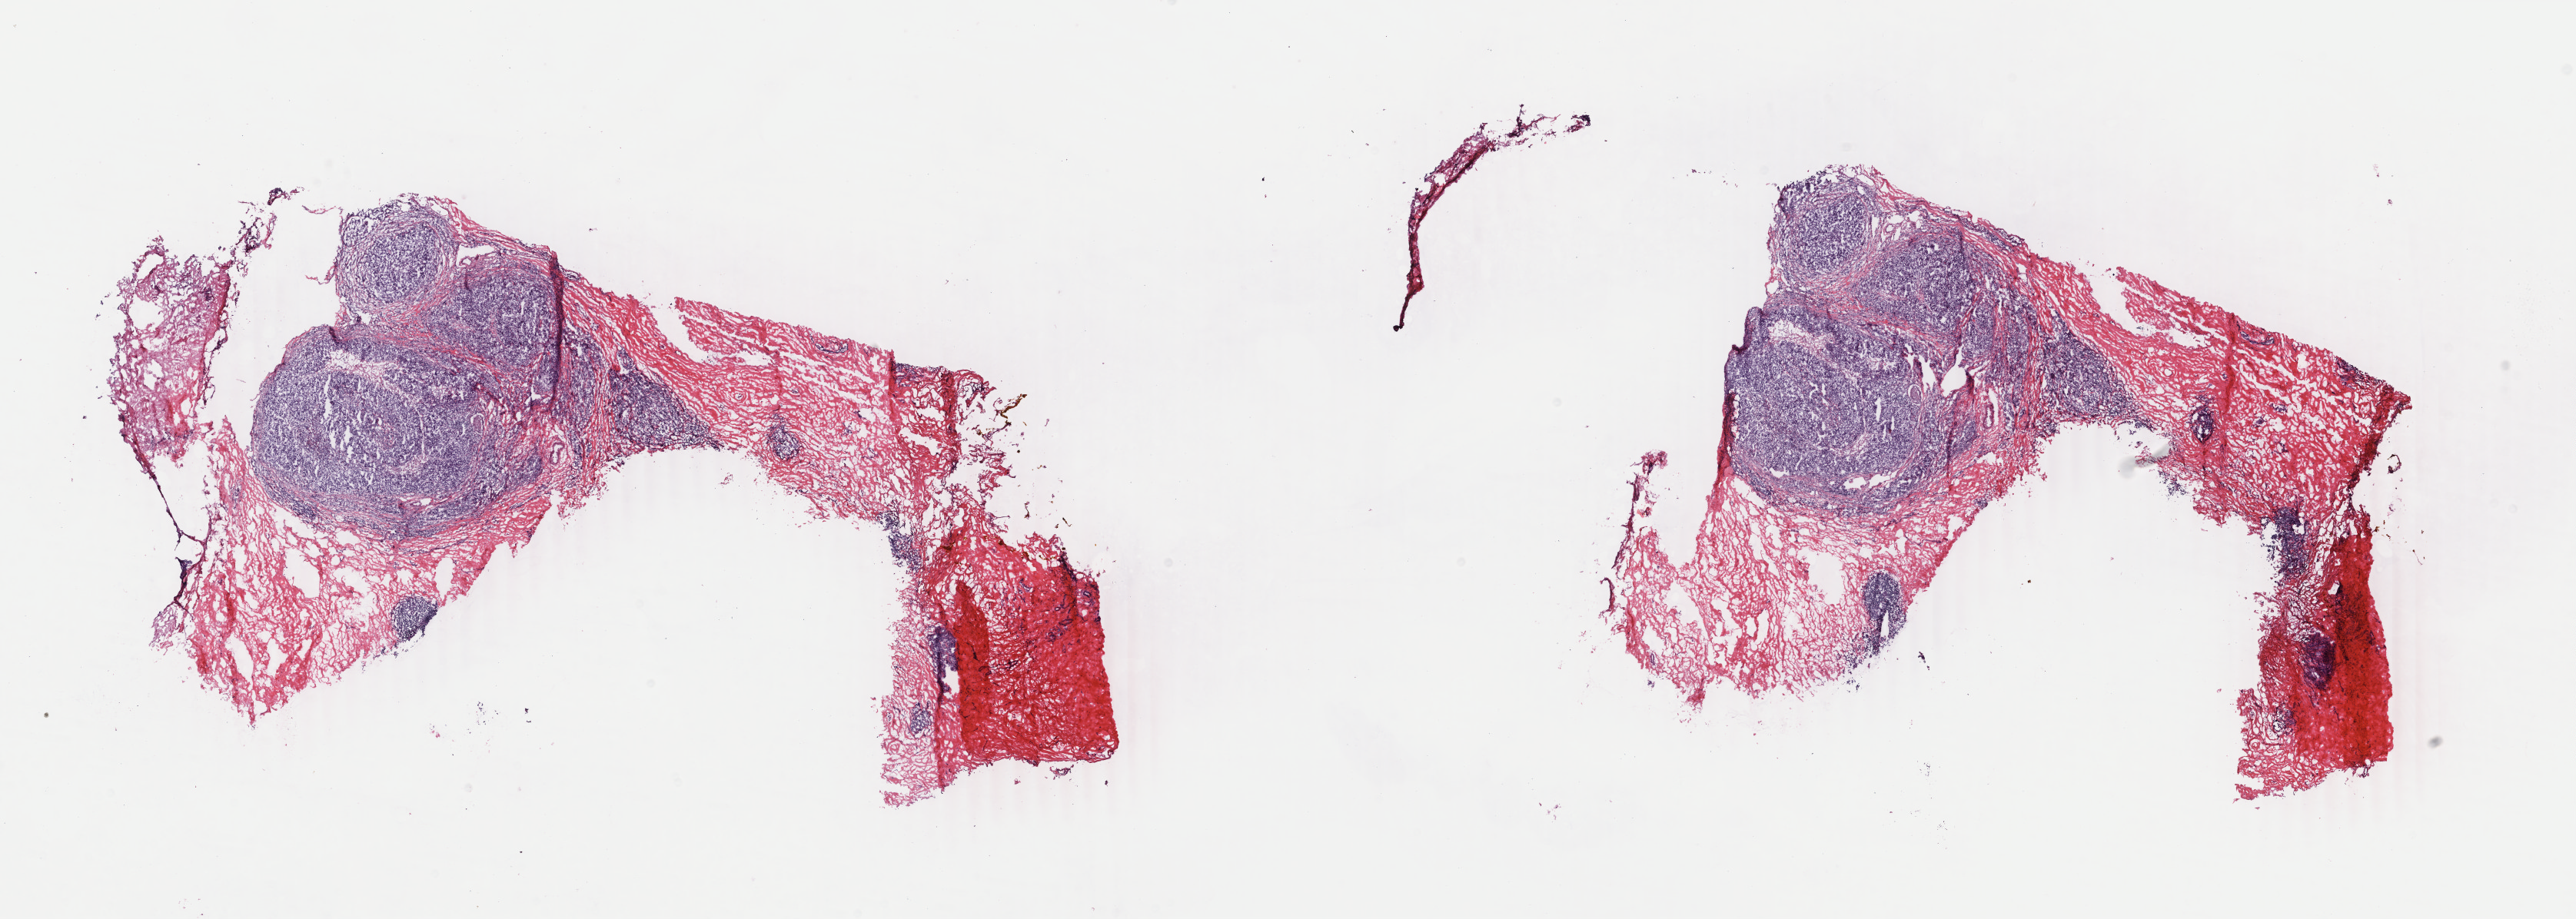
Whole-slide histology image, Hematoxylin and eosin (H&E) stained — low-resolution overview of the scanned area, about 26.7 x 9.5 mm (from a 40x scan), frozen section from the top of the tissue portion, breast, primary tumour sample. Female, age 62 years at initial diagnosis. Composition of this section per pathologist review: tumour cells 70%, tumour nuclei 85%.
Diagnosis: Infiltrating duct carcinoma, NOS.